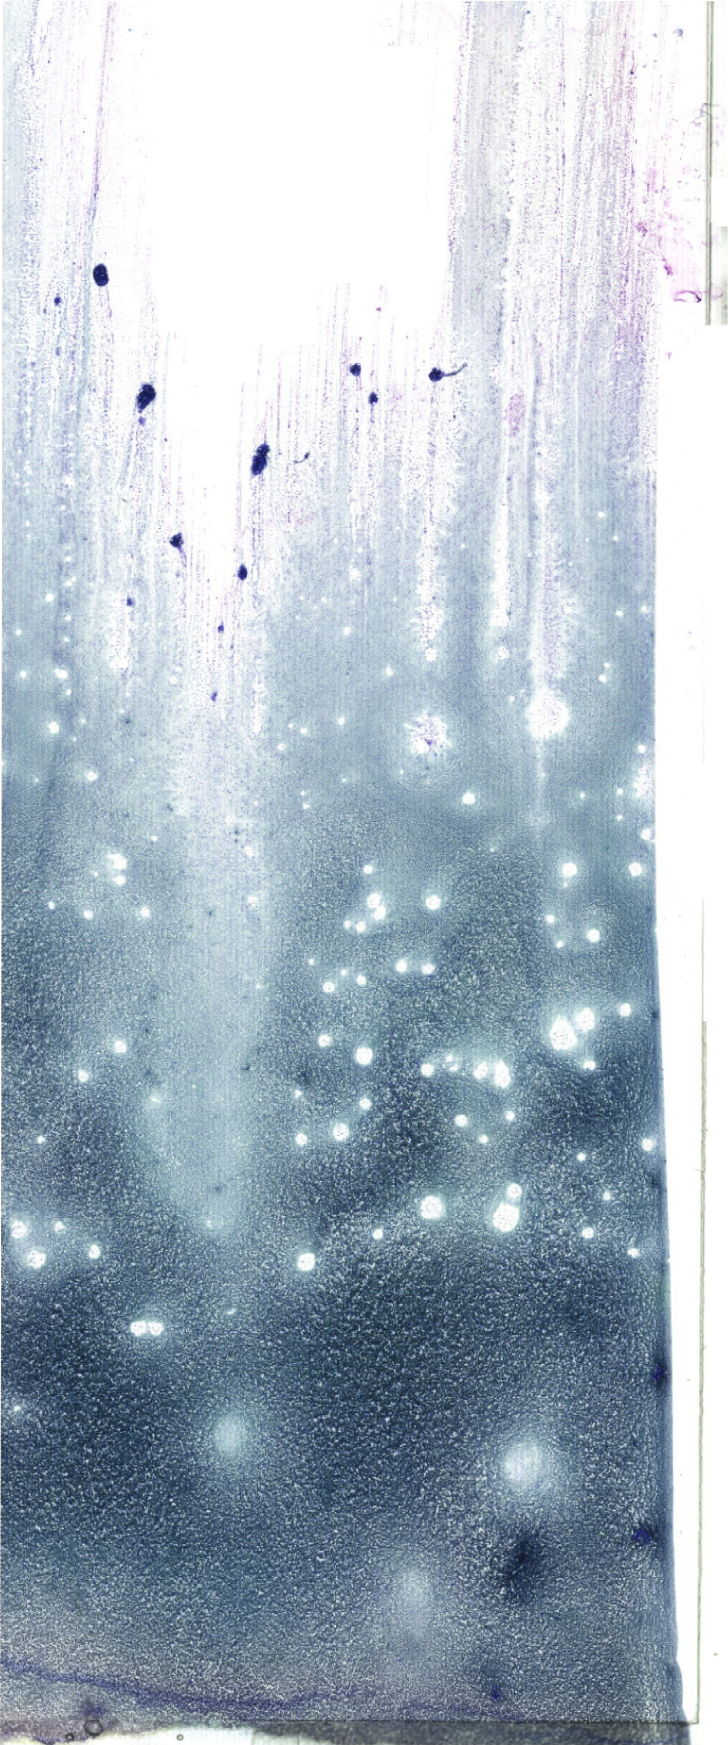
May-Grünwald–Giemsa-stained marrow aspirate smear (whole slide), a low-resolution overview of the entire scanned area, about 20.6 x 49.5 mm. Patient sex: male.
Diagnosis: T Acute Lymphoblastic Leukemia.